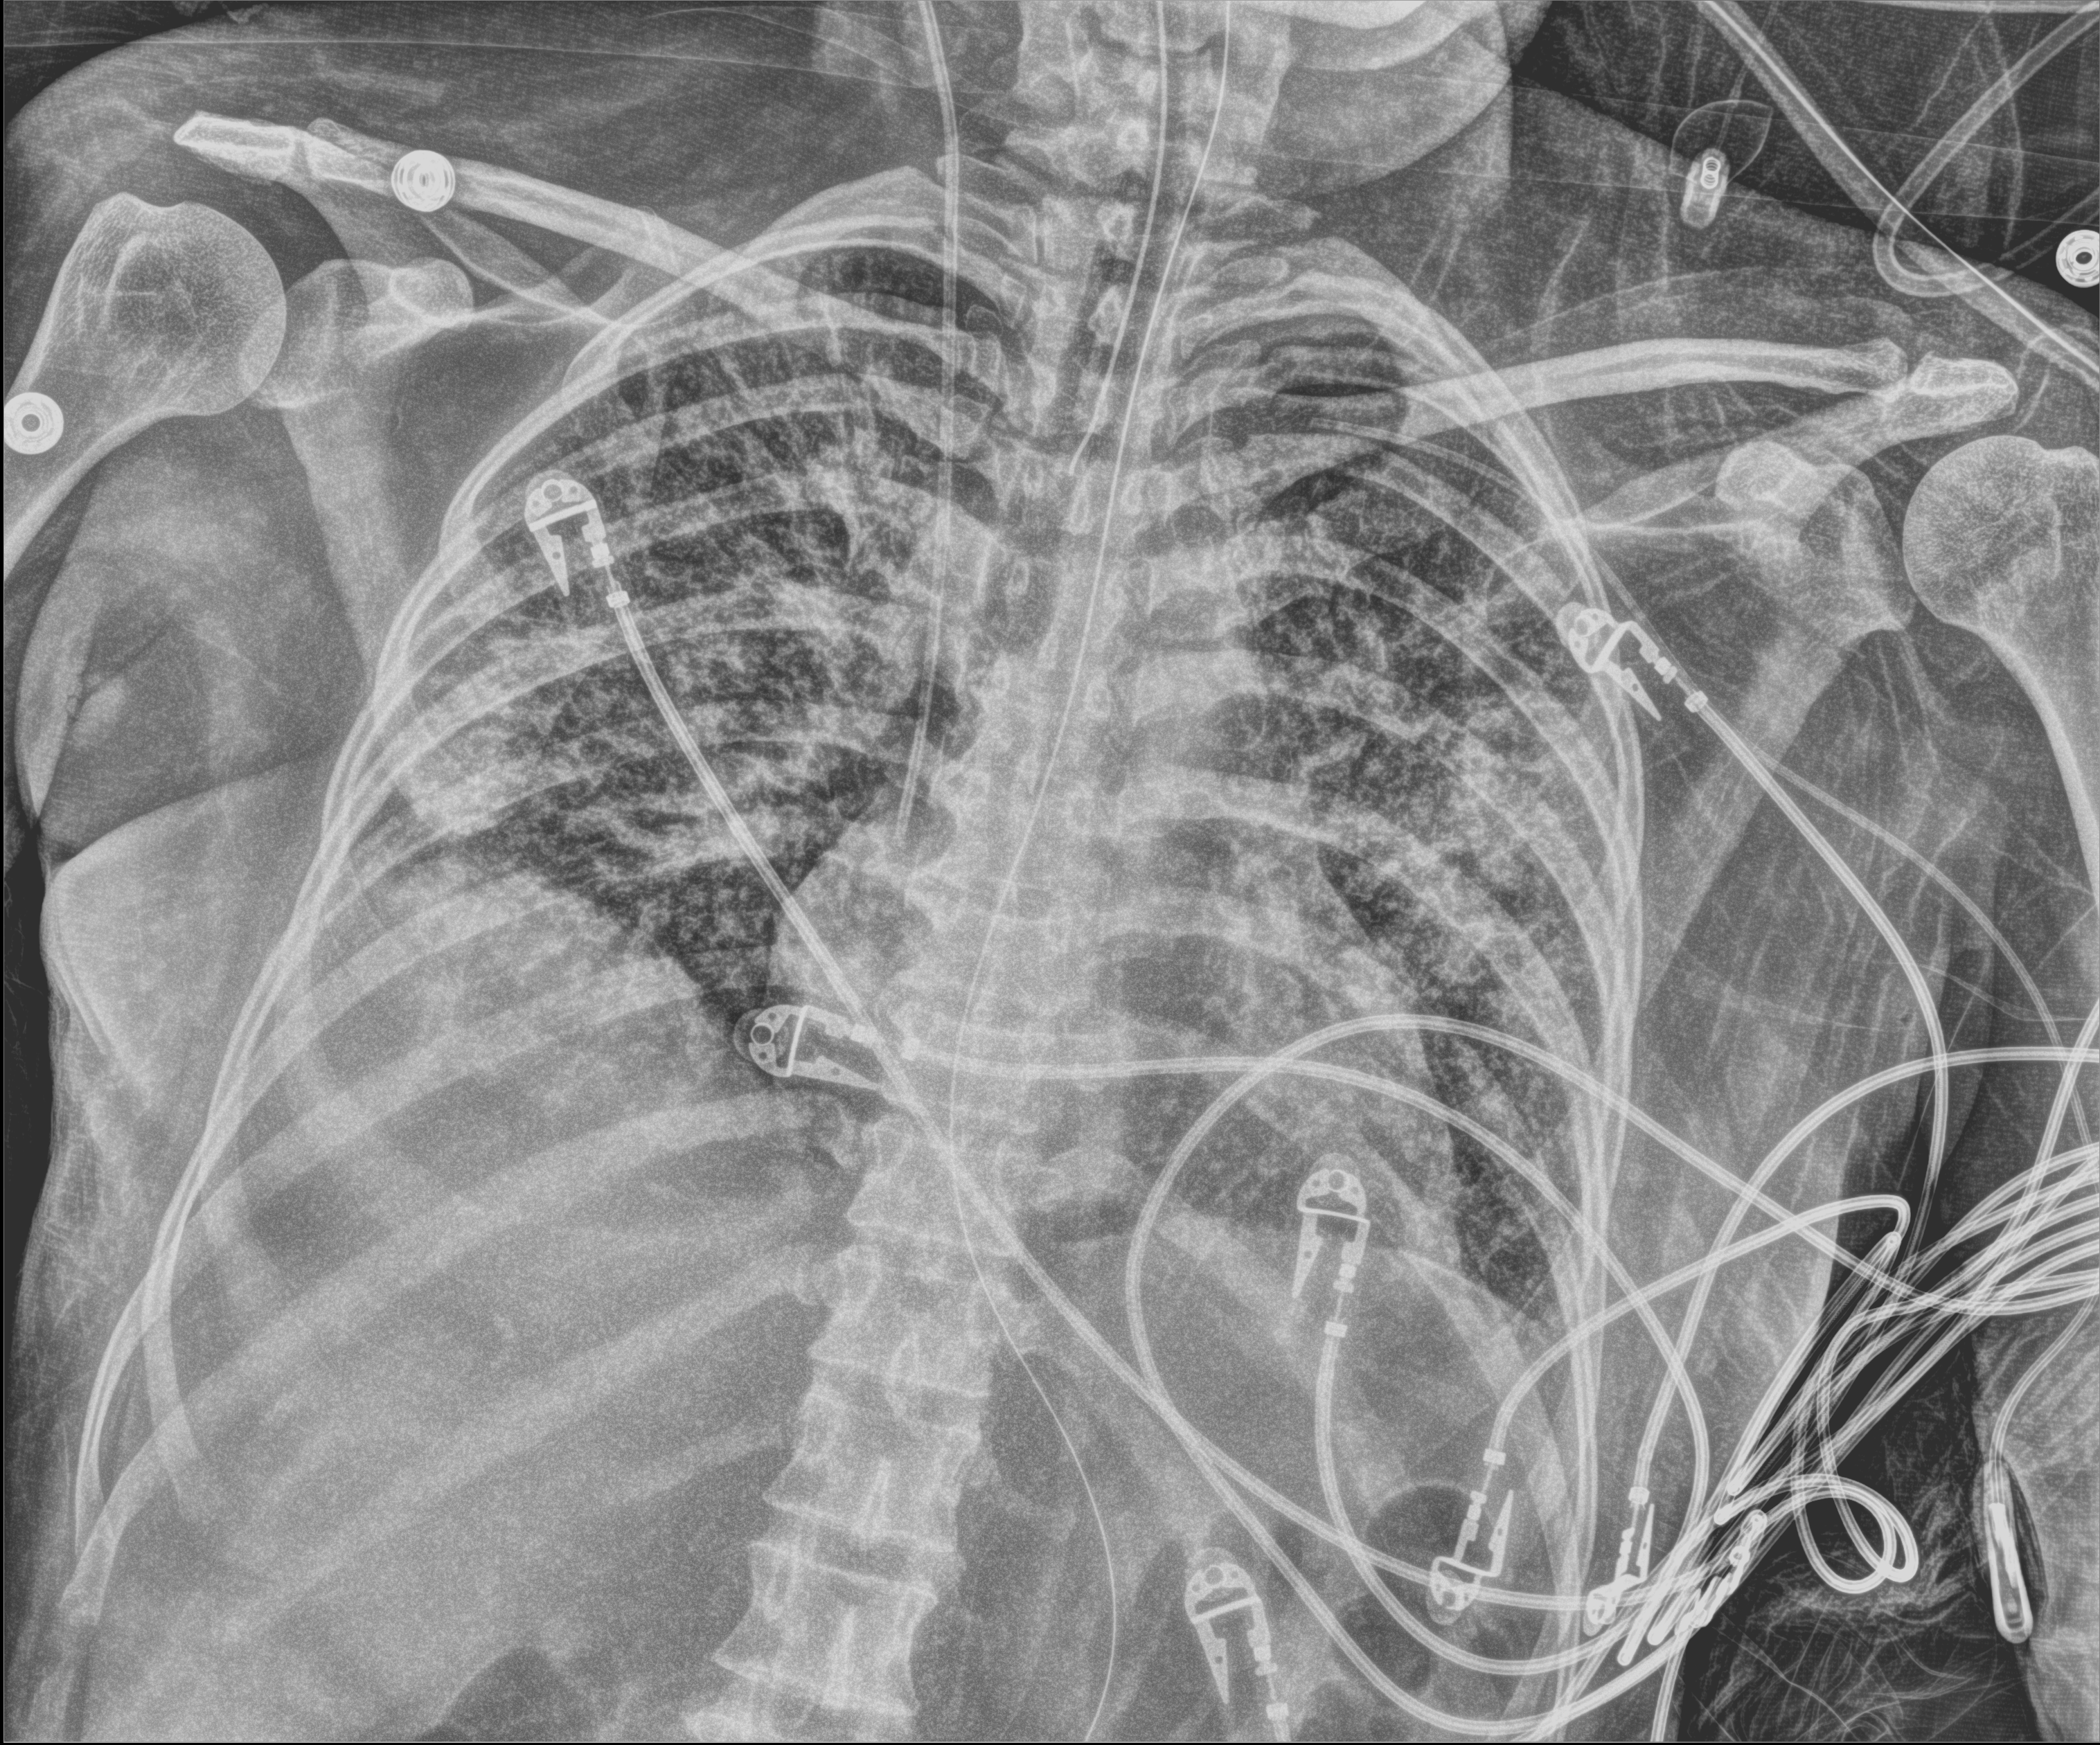
Portable chest radiograph, anteroposterior (AP) projection. Patient hospitalised with COVID-19; female, aged 18–59 years.
From the hospital-stay record, not from the radiograph (when in the stay this image was taken is not recorded): admitted to intensive care during this hospital stay: yes; diabetes (admission record): no; length of hospital stay: 71 days.